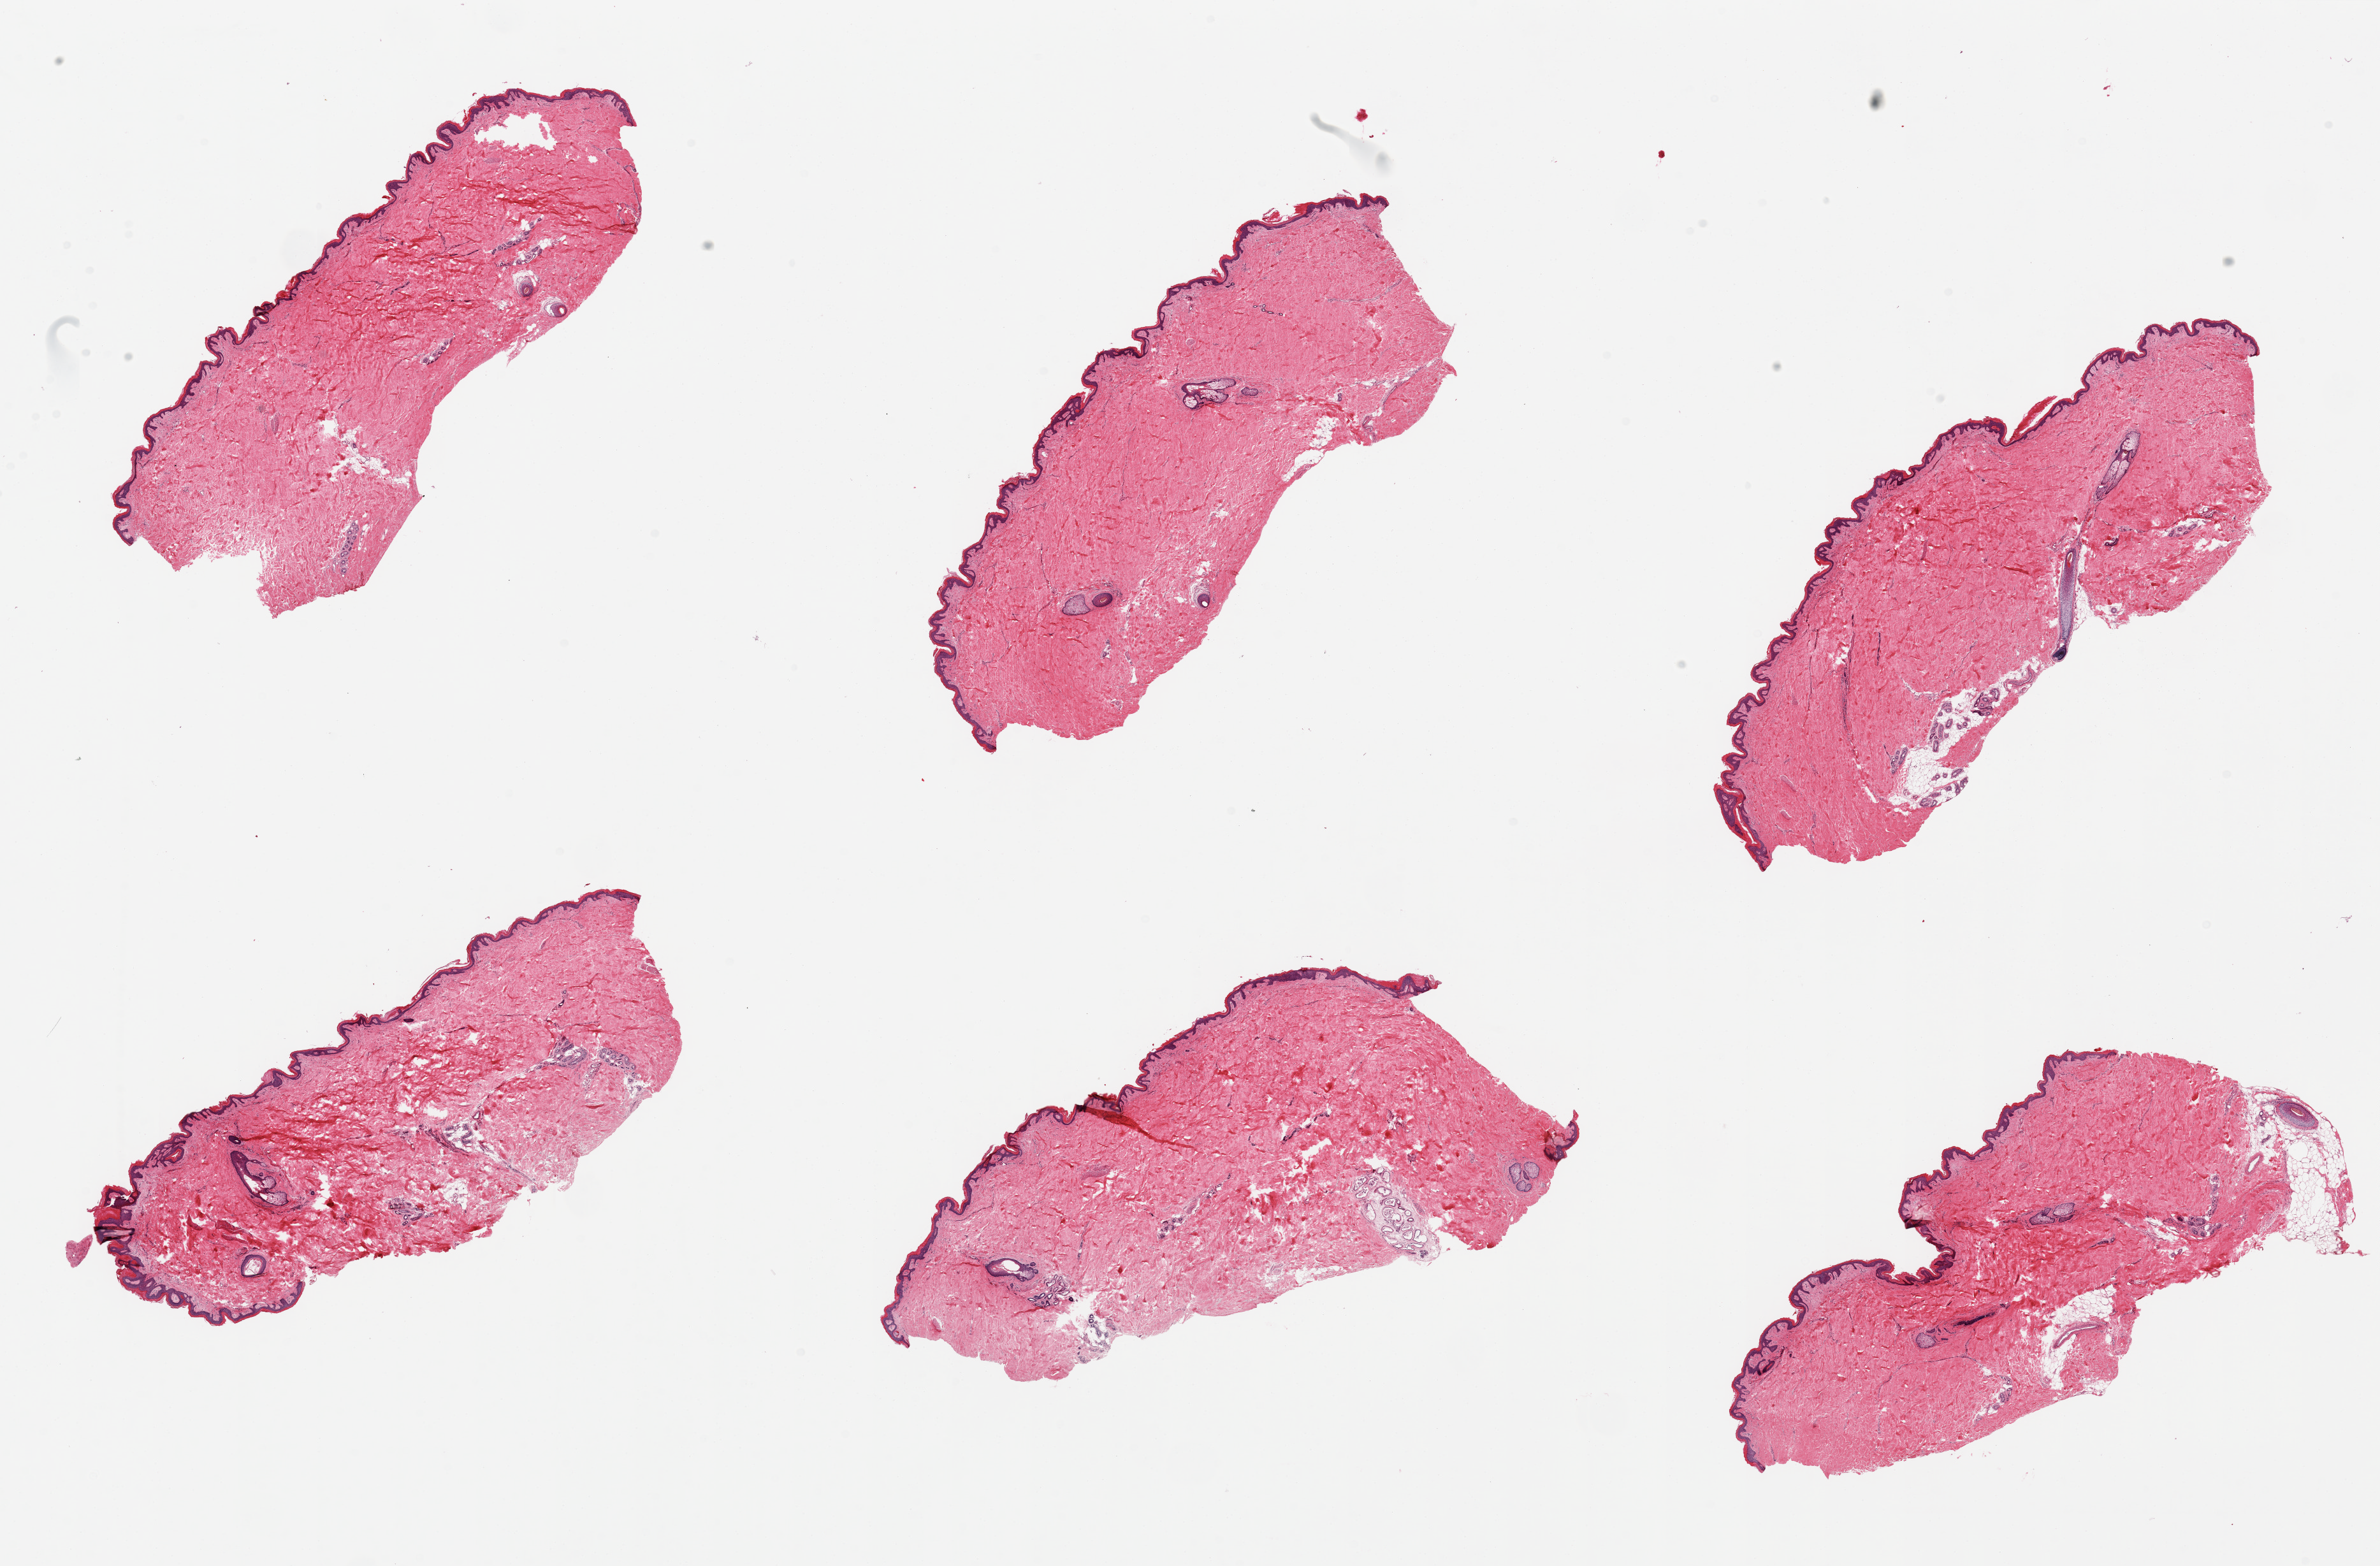
Digitized haematoxylin and eosin-stained section — low-resolution overview of the scanned area, about 29.5 x 19.4 mm; PAXgene-fixed, paraffin-embedded tissue; section of skin of suprapubic region (target tissue); tissue donor sample.
Review note (as recorded): 6 pieces, minimal dermal fat.